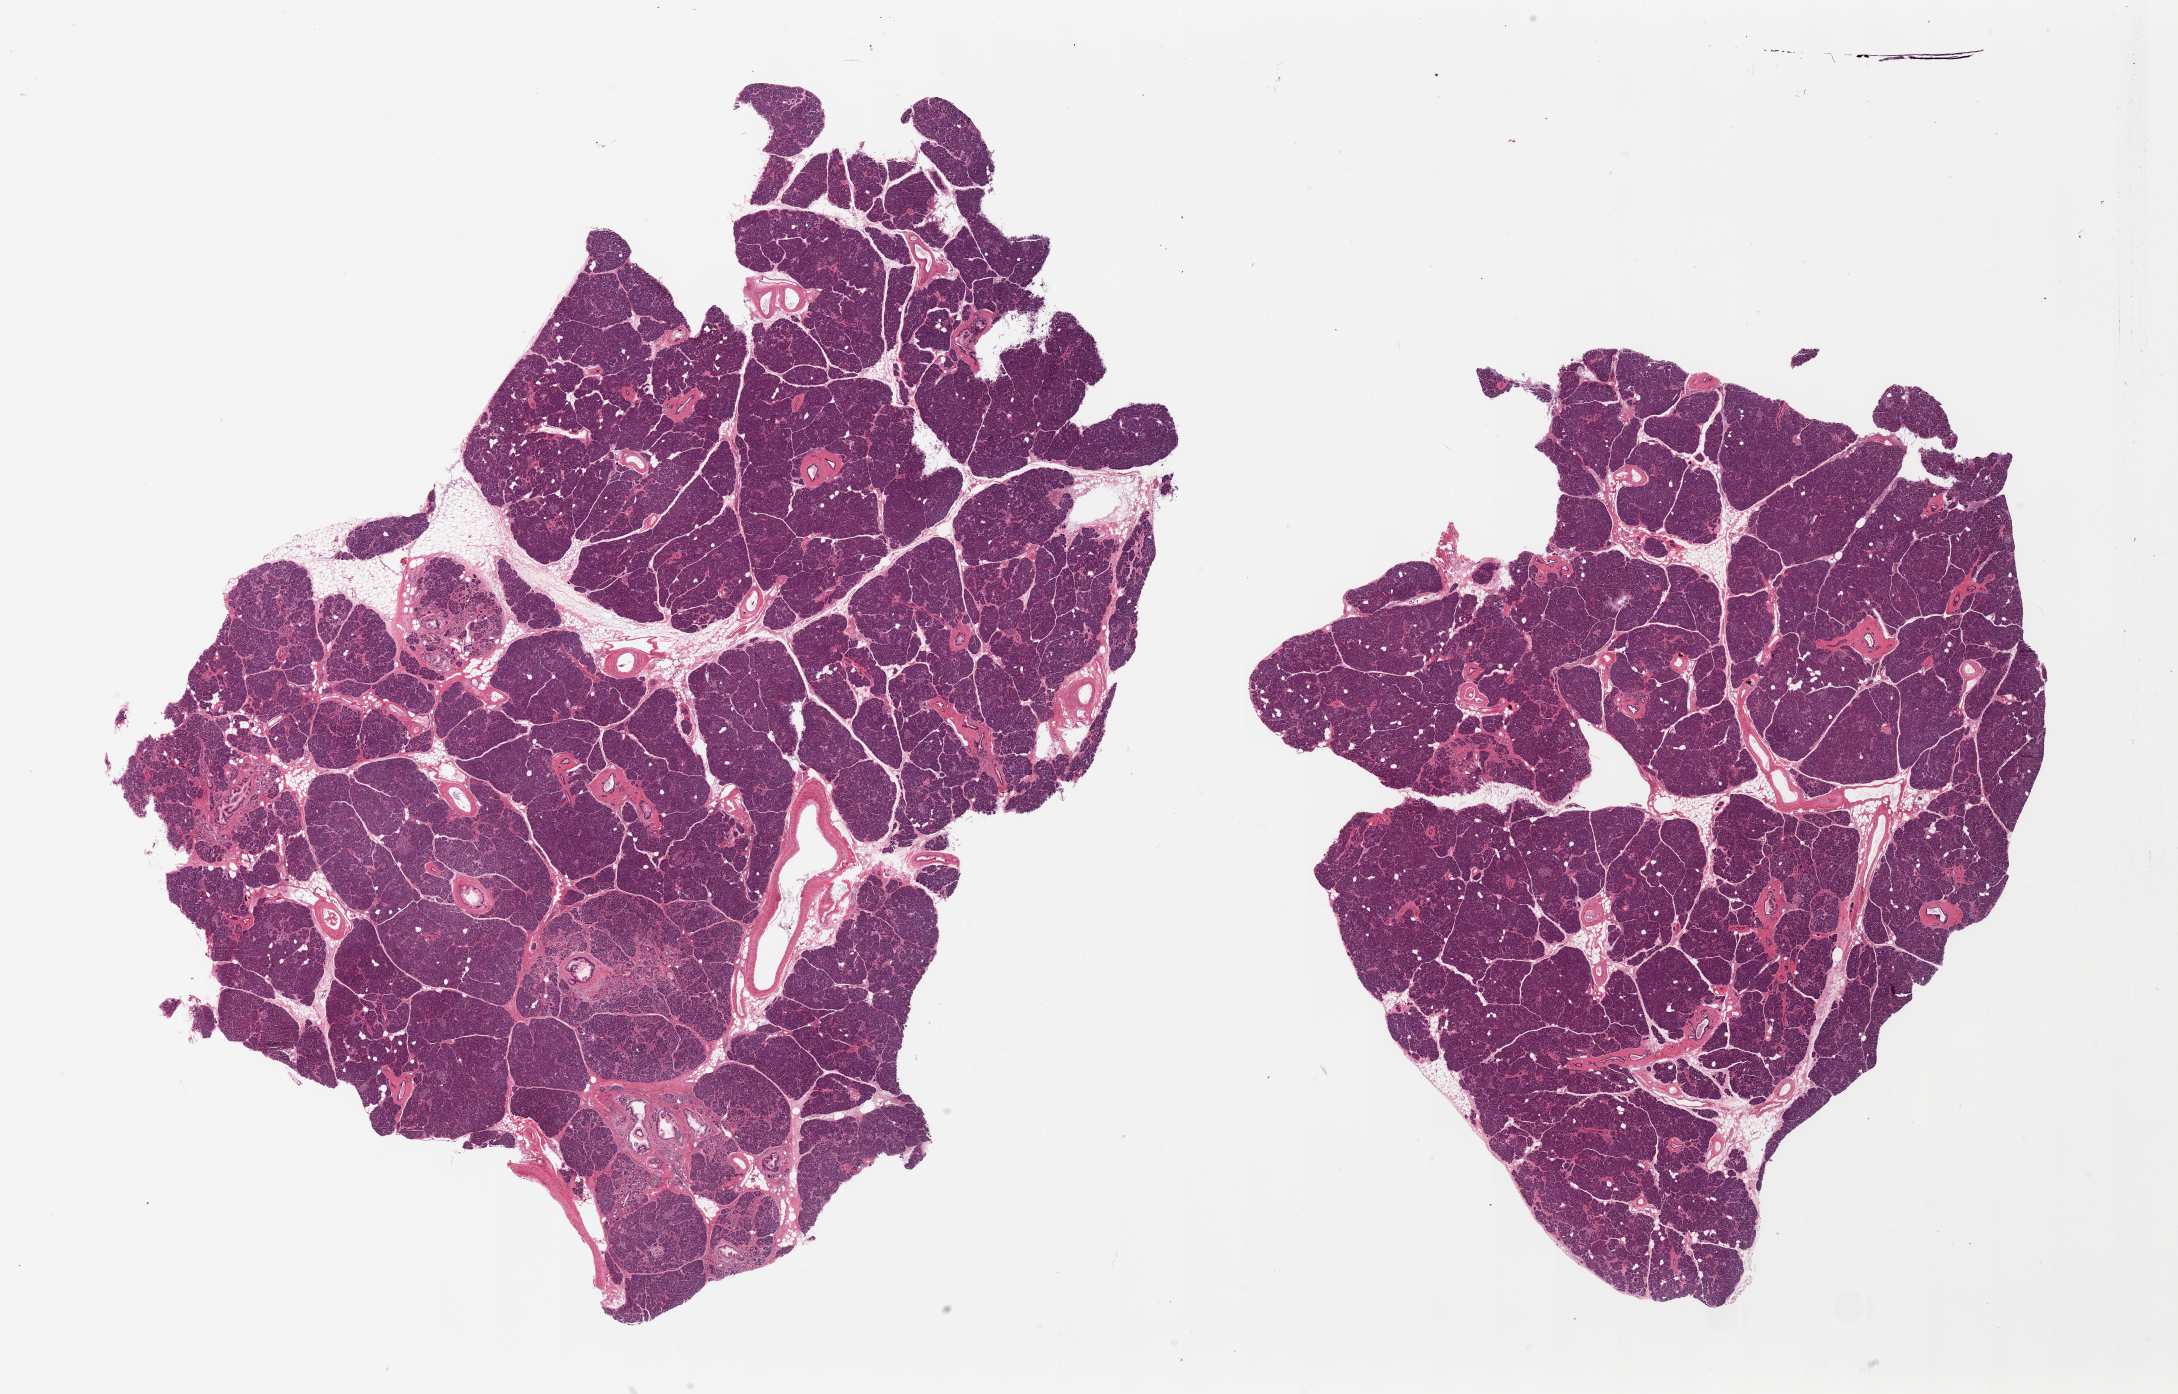
Haematoxylin and eosin whole-slide image, brightfield — a low-resolution overview of the entire scanned area, about 34.5 x 22.1 mm (acquisition: 20x scan), PAXgene-fixed, paraffin-embedded tissue, sampled site (target tissue): pancreas, donor tissue sample. Donor: male.
- review note (as recorded): 2 pieces. PanIN 1a. Scattered foci of fibrosis and atrophy